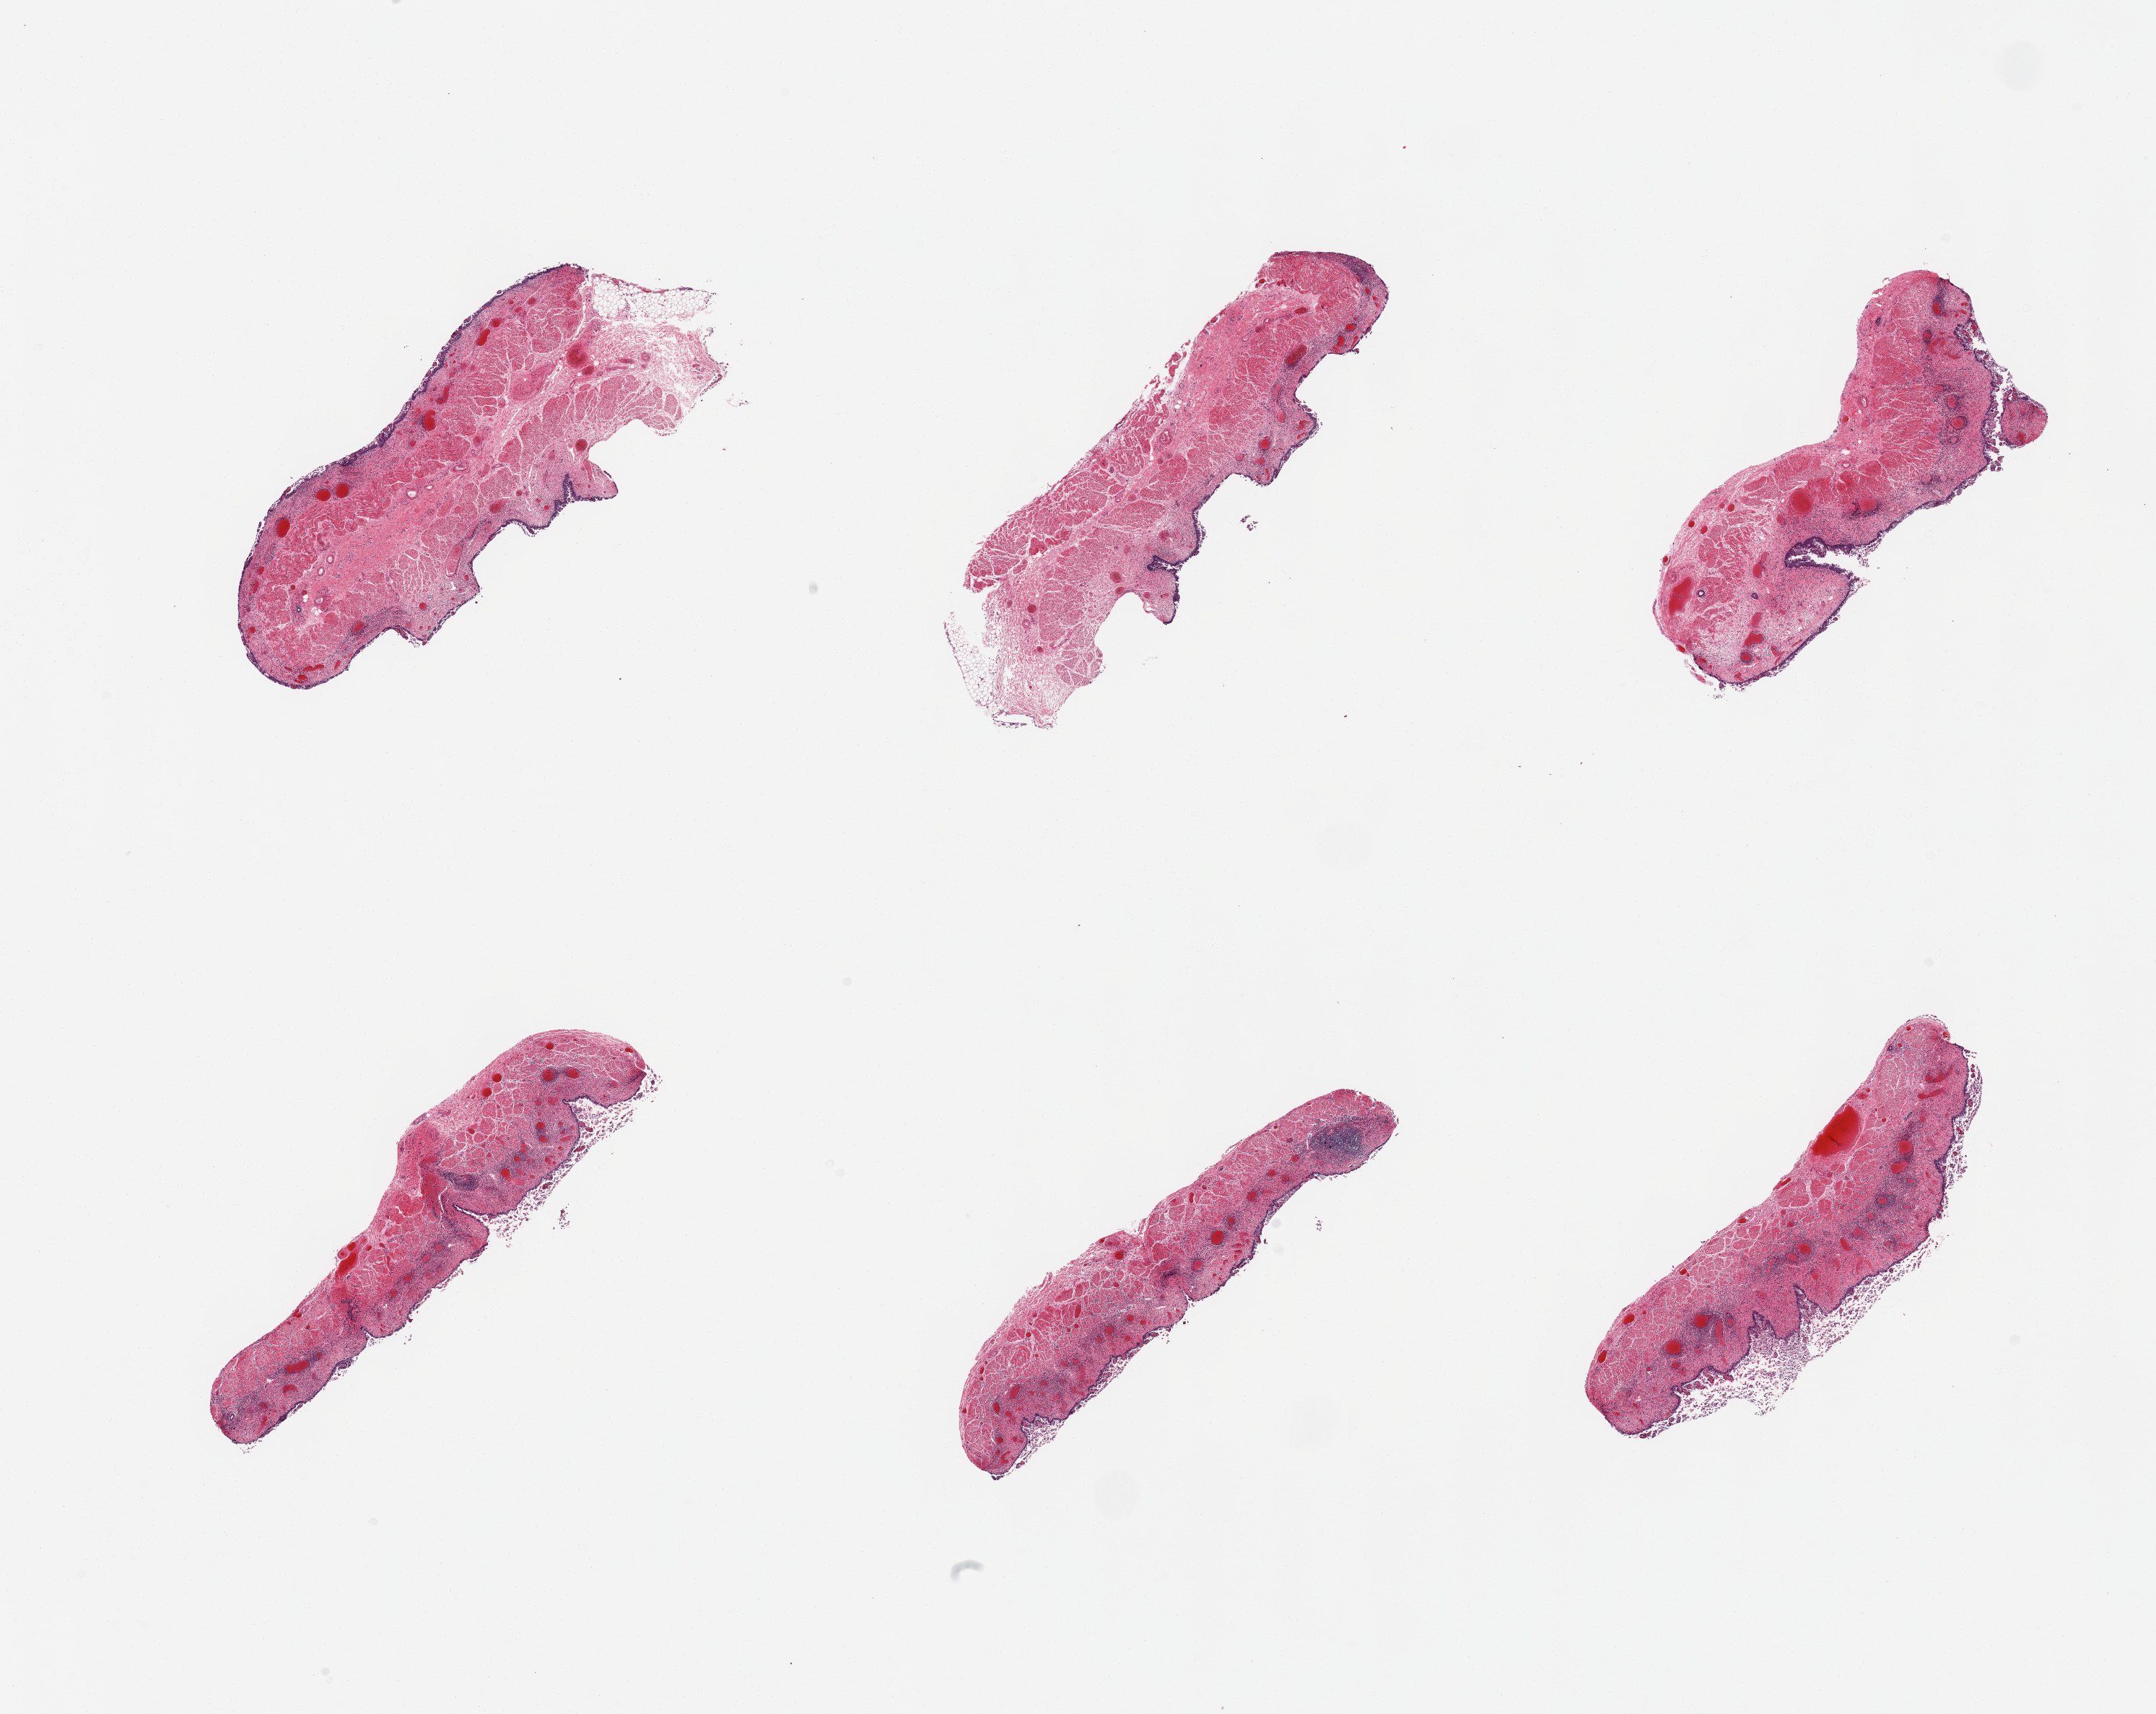
Hematoxylin and eosin (H&E) whole-slide image, brightfield, low-resolution overview of the scanned area, about 23.6 x 18.8 mm. PAXgene-fixed, paraffin-embedded tissue. Section of esophageal mucous membrane (target tissue). Donor tissue sample. Donor sex: male.
Reviewer comment on this tissue sample: 6 pieces, mucosa markedly and unusually autolyzed, sloughing, ~ 0.1mm residual, with chronic esophagitis.